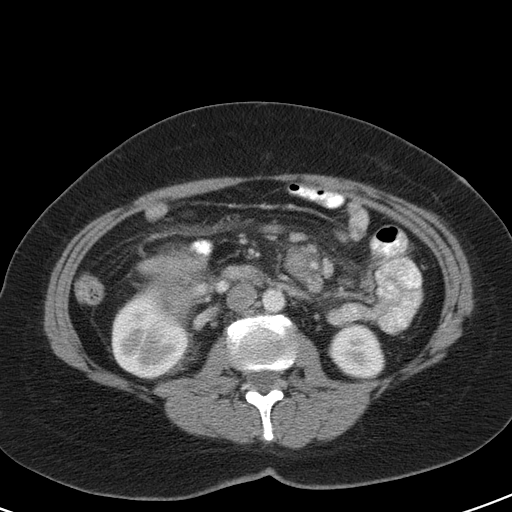
Contrast-enhanced abdominal CT, one axial slice; slice 57 of 126 in the series (ordered by position); intravenous contrast given; soft-tissue window (W 400 / L 40 HU); 512 × 512 image matrix. Patient: female, 51 years. From the clinical record (not read from this slice): diagnosis: adrenocortical carcinoma; tumour side: right adrenal; tumour size at pathology: 17 cm; Ki-67 index: 12 %; stage (as recorded): 2.
Outlined on this slice (semi-automatic segmentation, software-assisted and operator-edited):
- mass: bounding box (x1, y1, x2, y2) in pixels: (142, 250, 205, 316)